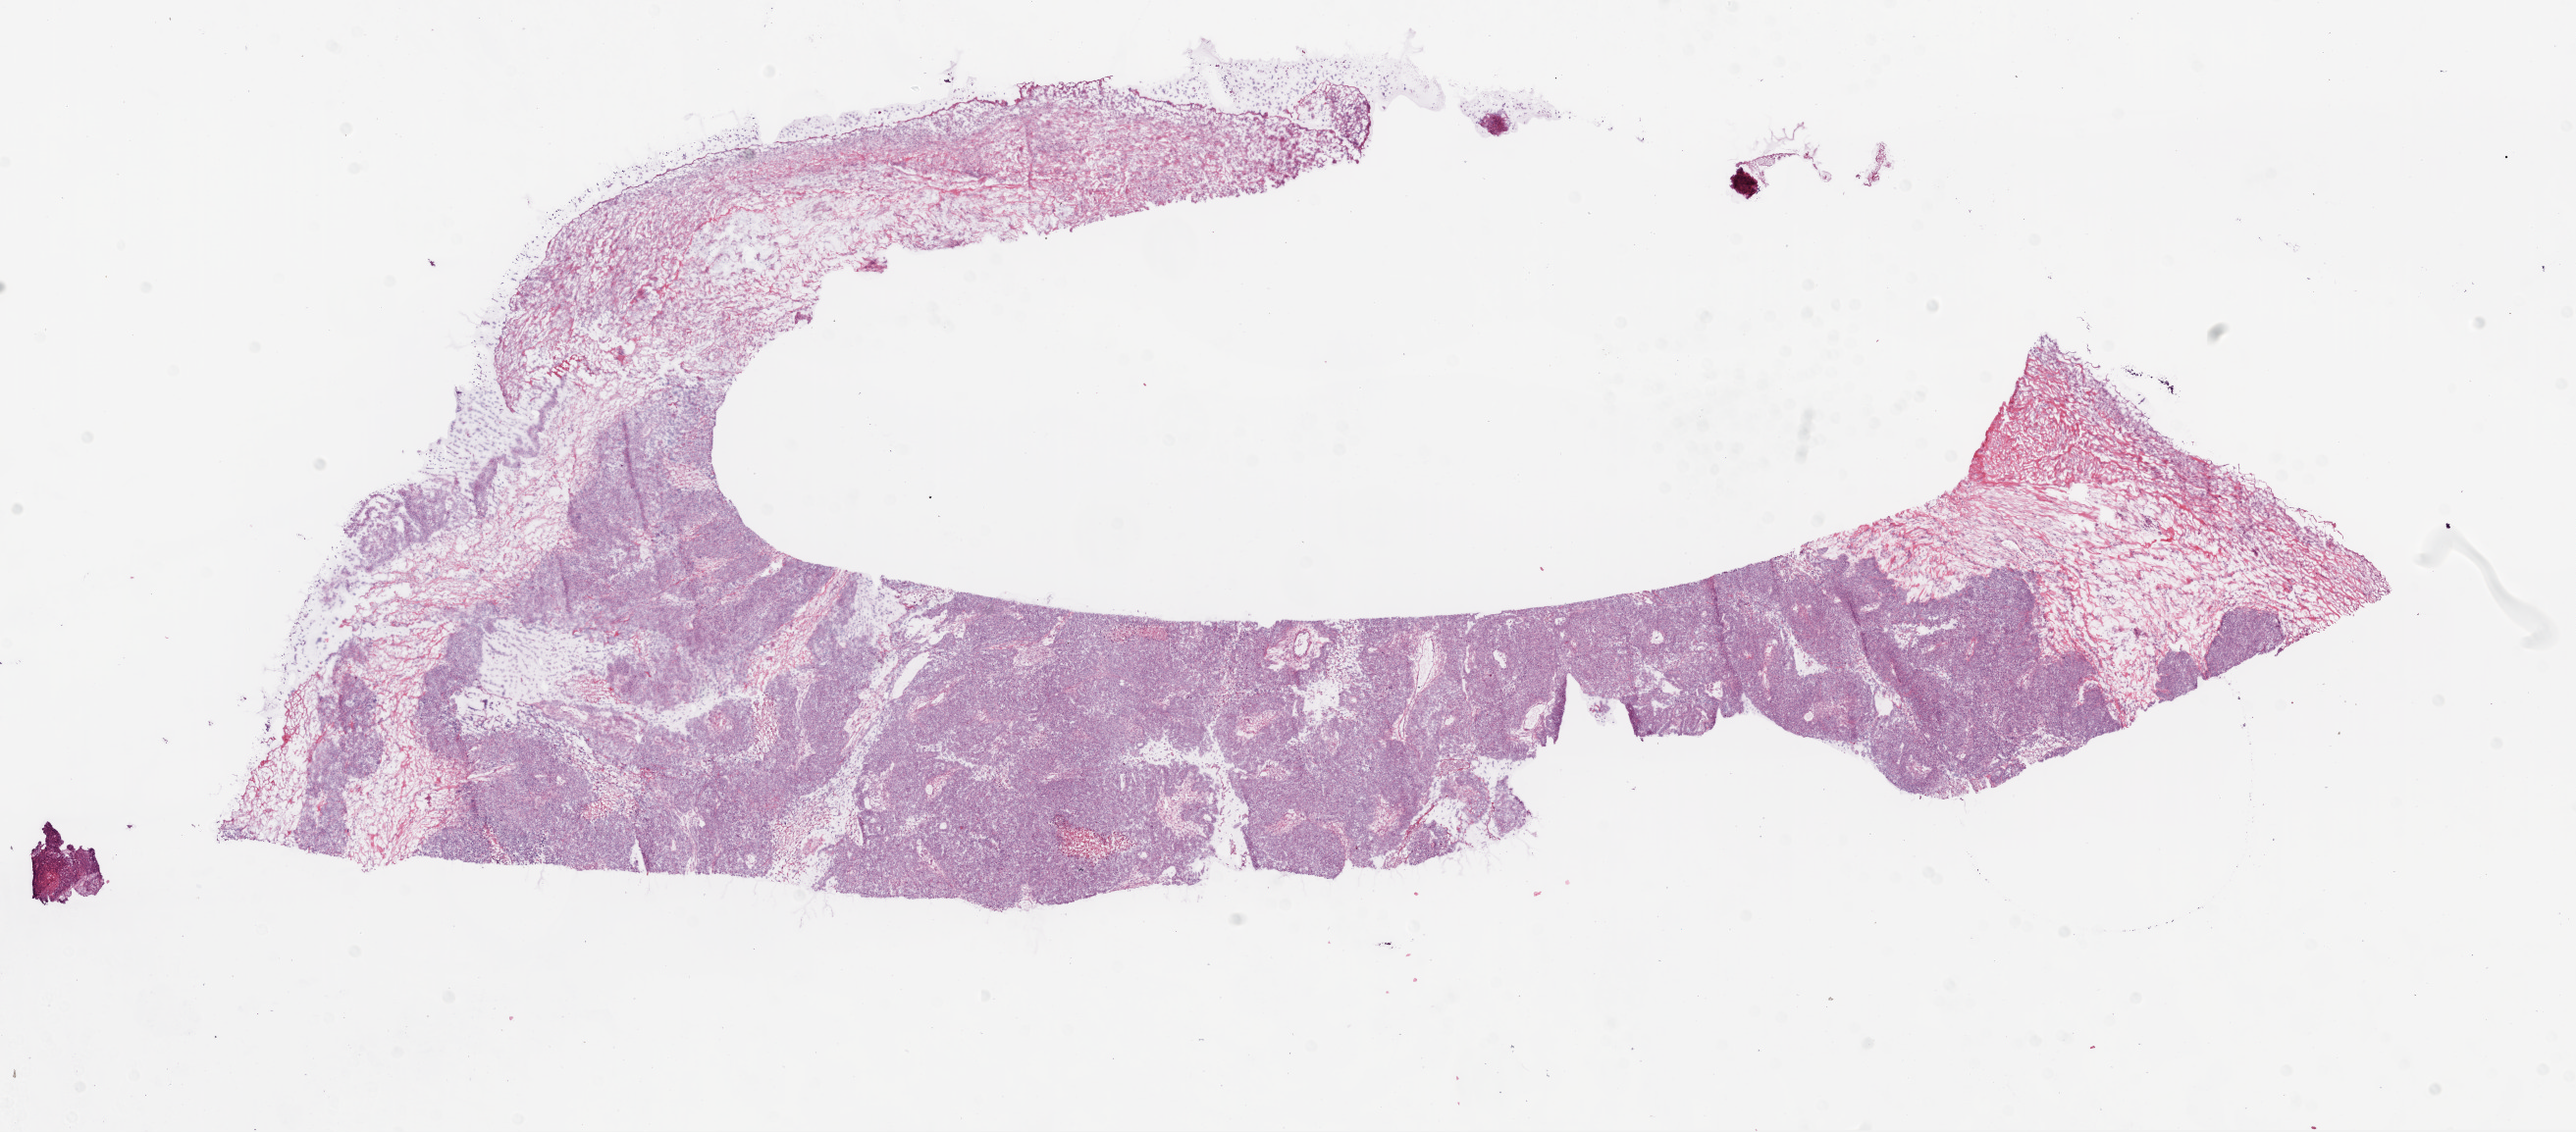
Hematoxylin and eosin (H&E) stained whole-slide image, whole scanned area (about 21.1 x 9.3 mm, from a 20x scan) shown as a low-resolution overview. Frozen section from the bottom of the tissue portion. Primary tumour sample from the ovary. Female, age 60 years at initial diagnosis. Histologic grade: G3 (poorly differentiated). Composition of this section per pathologist review: tumour cells 85%, tumour nuclei 90%, normal cells 0%, stromal cells 10%, necrosis 5%.
- FIGO stage: IIIB
- diagnosis: Serous cystadenocarcinoma, NOS